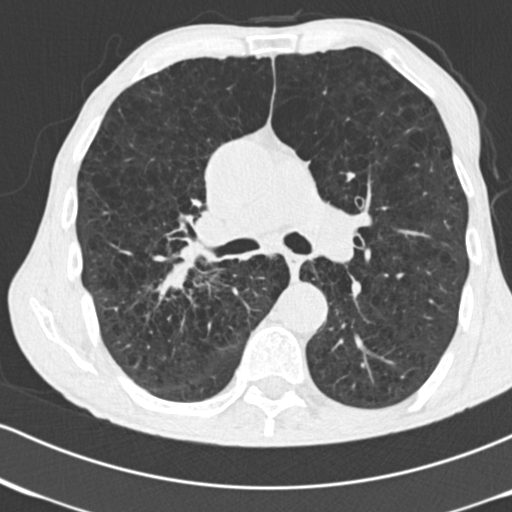
Low-dose screening chest CT, one axial slice; position 102 of 182 along the scan axis; 120 kVp; lung window (W 1500 / L -600 HU); 2 mm slice thickness; 512 × 512 image matrix.
Outlined on this slice (manually delineated by an expert):
- lesion 1 (tumor, lower lobe of right lung): bounding box <161,259,193,289> (left, top, right, bottom; pixels)